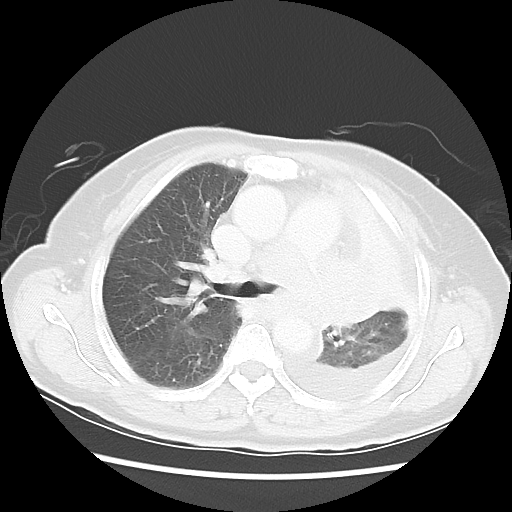
Chest CT, one axial slice. Position 35 of 52 along the scan axis. 120 kVp. Lung window (W 1500 / L -600 HU). 5 mm slice thickness. 512 × 512 image matrix, field of view 336 × 336 mm. Patient: female, 72 years. Case-level facts recorded for this patient, not image findings: clinical TNM (as recorded): T4 N3 M1b; histopathological grade: G3.
Outlined on this slice (rectangle marked by the reading radiologist):
- lung tumour (recorded histology: large cell carcinoma): bounding box <278,253,387,335> (left, top, right, bottom; pixels)